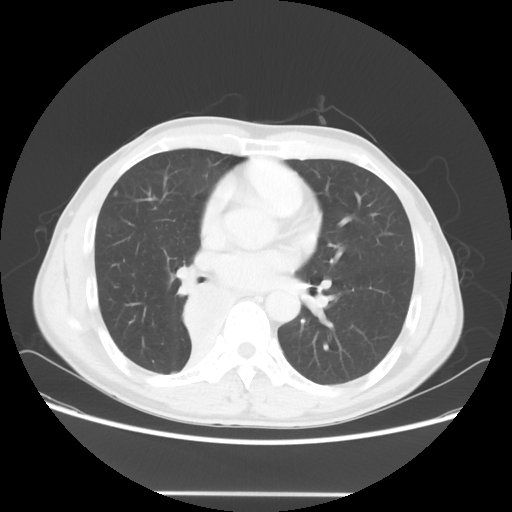
Chest CT, one axial slice. Slice 31 of 62 in the series (ordered by position). Reconstruction kernel STANDARD. 120 kVp. Lung window (W 1500 / L -600 HU). 512 × 512 image matrix, field of view 393 × 393 mm. Patient: male, 47 years. Case-level facts recorded for this patient, not image findings: clinical TNM (as recorded): T2 N0 M0; histopathological grade: G2.
Outlined on this slice (rectangle marked by the reading radiologist):
- lung tumour (recorded histology: squamous cell carcinoma): bounding box <178,282,249,361> (left, top, right, bottom; pixels)